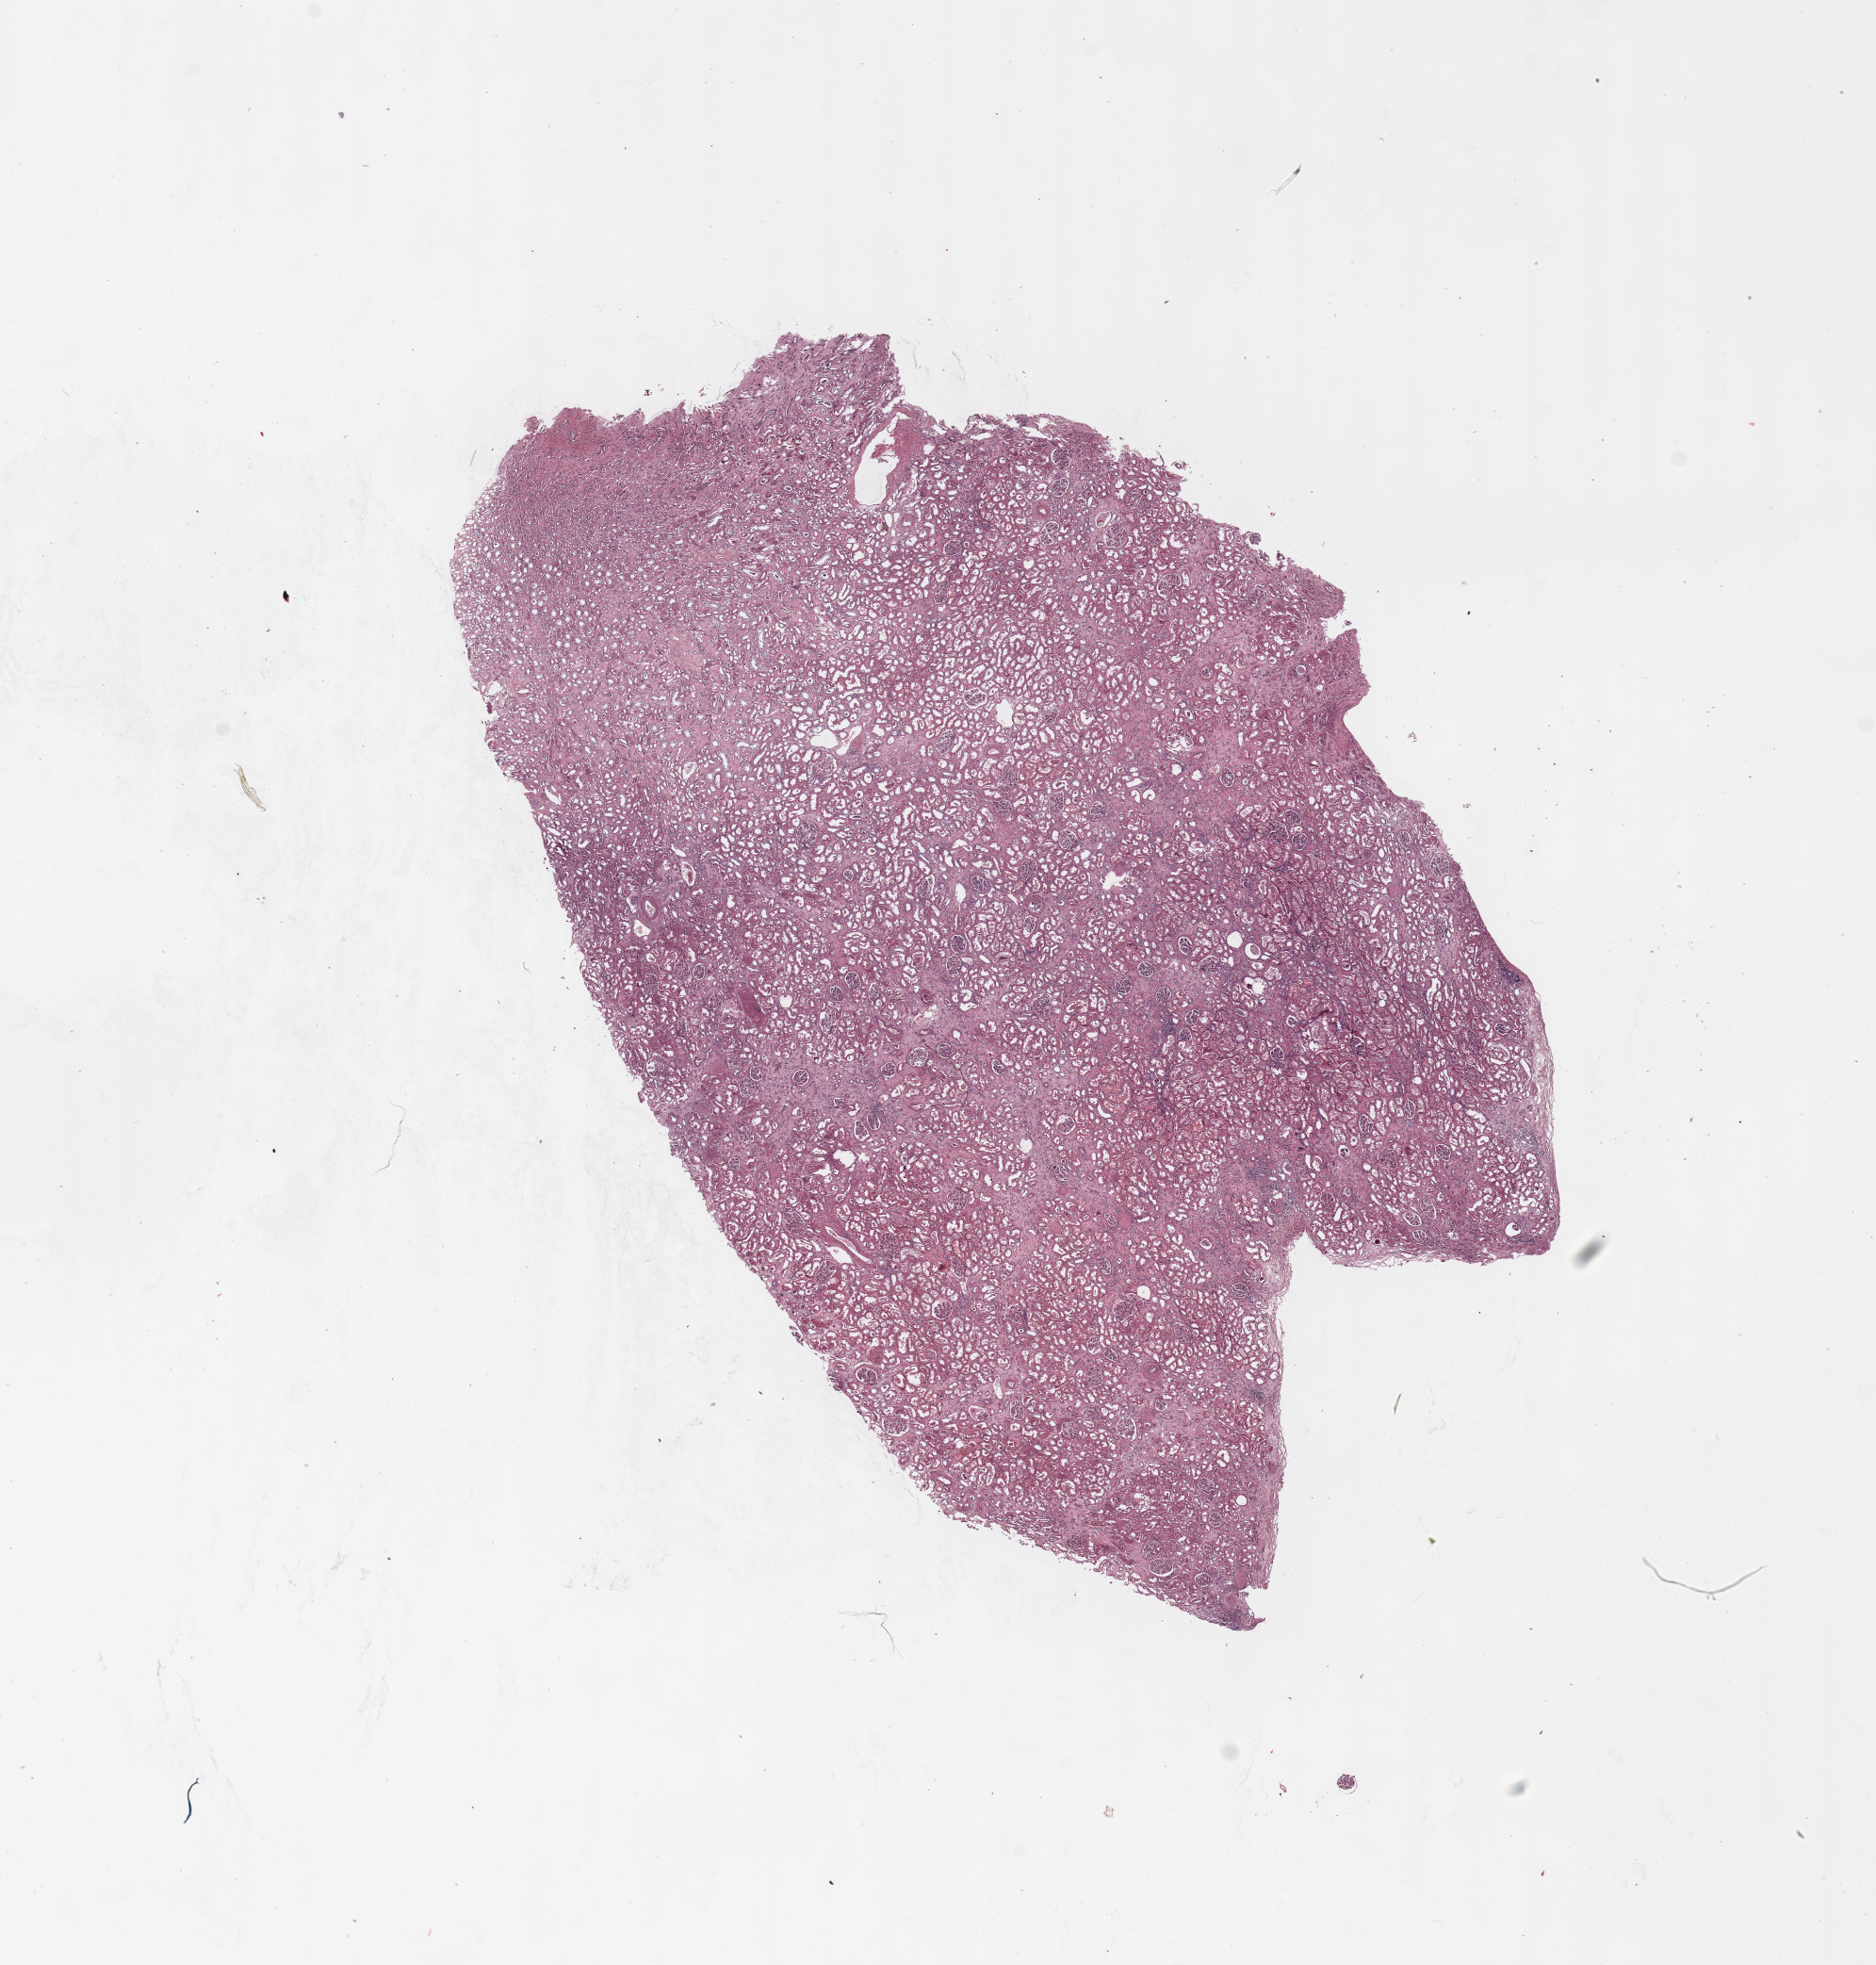
Whole-slide histology image, Hematoxylin and eosin (H&E) stained, shown as a low-resolution overview of the whole scanned area (about 15.8 x 16.5 mm, acquisition: 20x scan), kidney, normal (non-tumour) tissue. 68-year-old male patient.
This section: normal (non-tumour) tissue from the same patient. Patient diagnosis: Renal cell carcinoma, NOS.